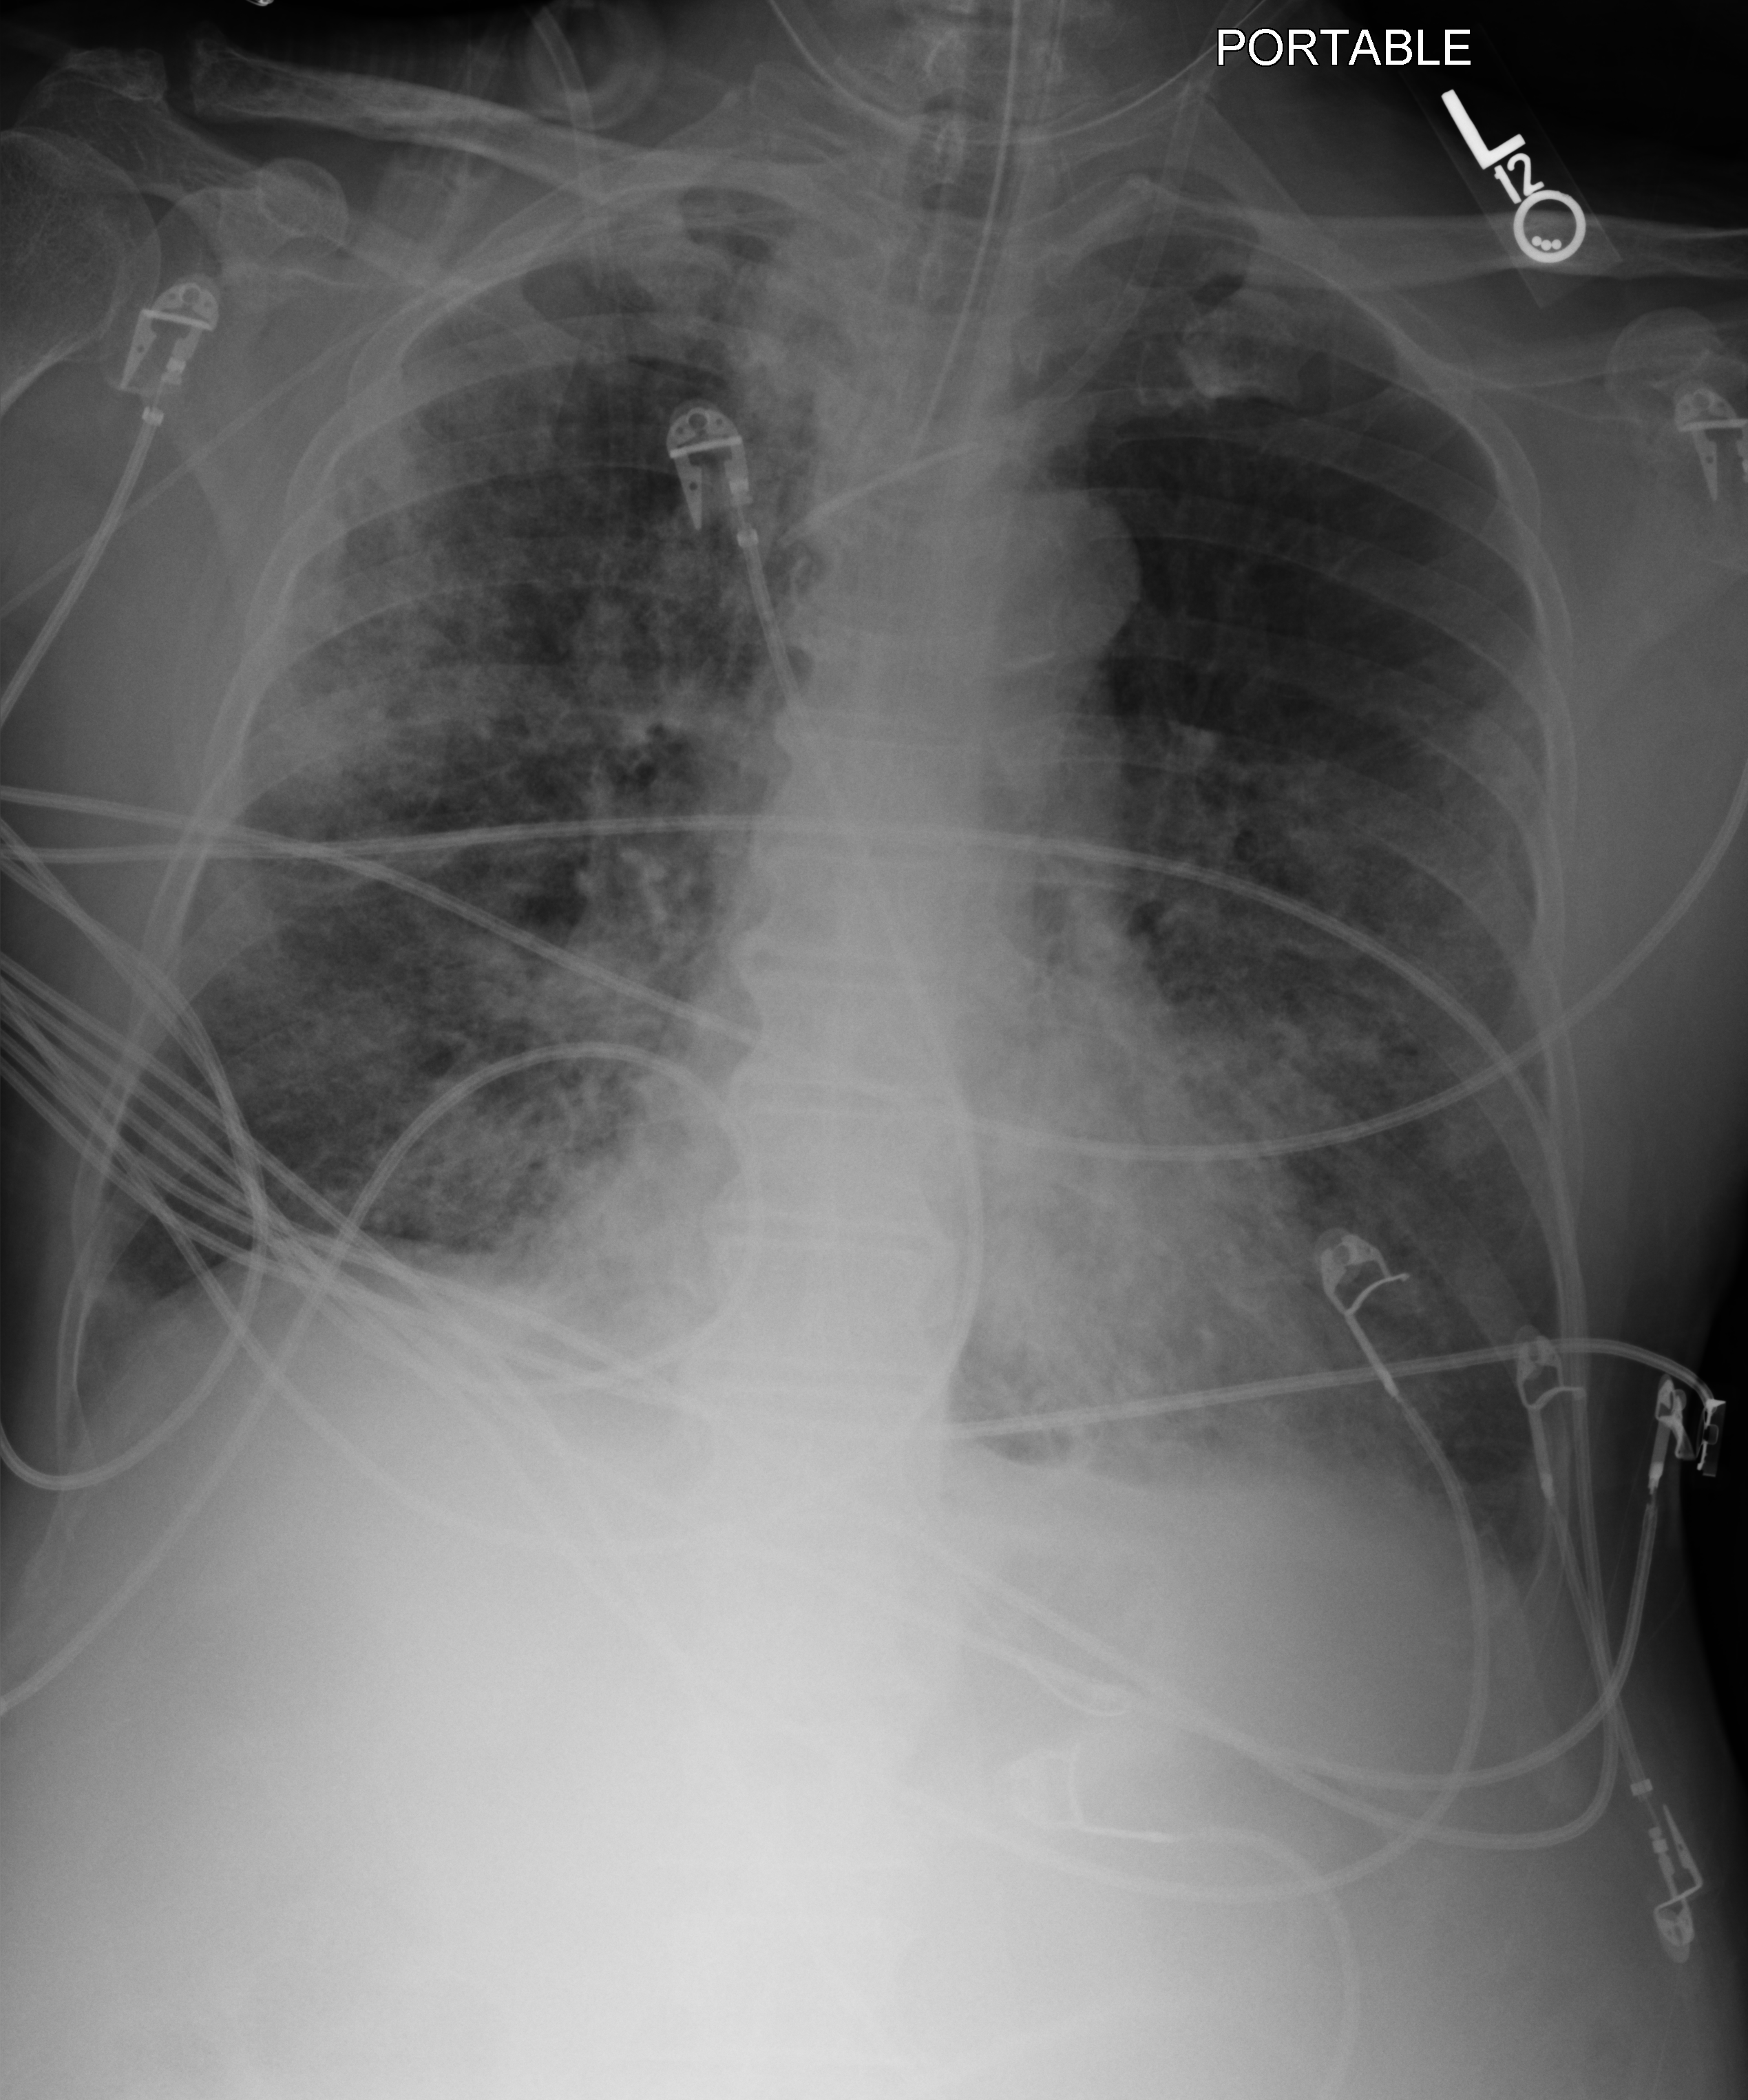
Chest X-ray (portable), anteroposterior (AP) projection. Male patient hospitalised with COVID-19, age 60–74 years.
Admission-level facts for this patient (not findings on this image; timing relative to this image not recorded): smoking status (admission record): never.